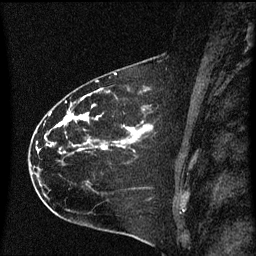
Breast MRI (dynamic contrast-enhanced), one sagittal slice. Position 39 of 60 along the scan axis. Dynamic contrast-enhanced series, image 2 of 3 at this slice position (ordered by acquisition). 1.5 T. TE 4.2 ms, TR 8.4 ms. 256 × 256 image matrix, field of view 200 × 200 mm. Patient: female, 35 years. From the clinical record (not read from this slice): setting: breast cancer imaged before/during neoadjuvant chemotherapy; receptor status: HER2-positive.
Outlined on this slice (semi-automatically segmented with operator editing):
- analysis volume of interest (the breast-tissue region the enhancement analysis was run in; not a lesion): box from (x=31, y=68) to (x=173, y=173) px
- tumour enhancement mask (voxels above the 70 % enhancement threshold inside the analysis volume of interest): (x=49, y=98)–(x=151, y=151)